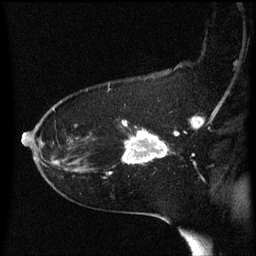
Breast MRI (dynamic contrast-enhanced), one sagittal slice. Position 42 of 60 along the scan axis. Dynamic contrast-enhanced series, image 2 of 3 at this slice position (ordered by acquisition). 1.5 T. TE 4.2 ms, TR 8.4 ms. 2 mm slice thickness. 256 × 256 image matrix, field of view 200 × 200 mm. Patient: female, 54 years. Case-level facts recorded for this patient, not image findings: setting: breast cancer imaged before/during neoadjuvant chemotherapy; receptor status: HR-positive, HER2-negative.
Structures marked on this image (semi-automatically segmented with operator editing):
- analysis volume of interest (the breast-tissue region the enhancement analysis was run in; not a lesion): bounding box (x1, y1, x2, y2) in pixels: (123, 122, 171, 165)
- tumour enhancement mask (voxels above the 70 % enhancement threshold inside the analysis volume of interest): (124, 130, 169, 165)